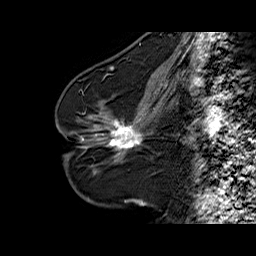
Breast MRI (dynamic contrast-enhanced), one sagittal slice. Position 30 of 60 along the scan axis. Dynamic contrast-enhanced series, time point 2 of 6 at this slice position (early post-contrast). 1.5 T. TE 6.3 ms, TR 32.5 ms. 4 mm slice thickness. 256 × 256 image matrix, field of view 200 × 200 mm. Female patient. From the clinical record (not read from this slice): setting: breast cancer imaged before/during neoadjuvant chemotherapy; receptor status: HR-positive, HER2-negative.
Outlined on this slice (semi-automatic segmentation, software-assisted and operator-edited):
- analysis volume of interest (the breast-tissue region the enhancement analysis was run in; not a lesion): bounding box <94,103,161,164> (left, top, right, bottom; pixels)
- tumour enhancement mask (voxels above the 100 % enhancement threshold inside the analysis volume of interest): <109,120,142,149>